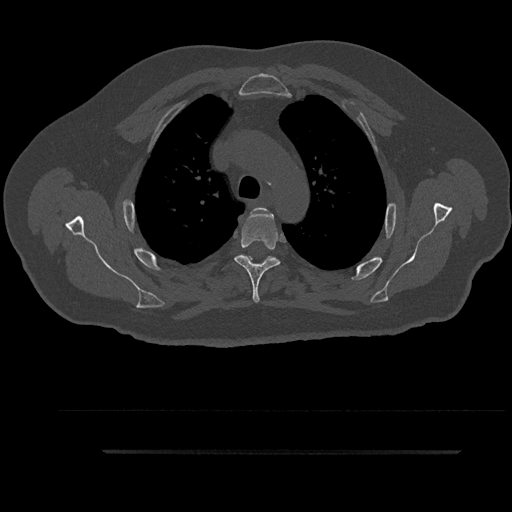
CT including the spine, one axial slice. Slice 670 of 797 in the series (ordered by position). Bone window (W 1800 / L 400 HU). 0.5 mm slice thickness. 512 × 512 image matrix, field of view 432 × 432 mm. Male patient, age 63 years. From the clinical record (not read from this slice): primary cancer: renal; vertebrae with lytic lesions (as recorded): T8.
Outlined on this slice (semi-automatically segmented with operator editing):
- T3 vertebra: bounding box <247,208,260,259> (left, top, right, bottom; pixels)
- T4 vertebra: <235,209,281,303>